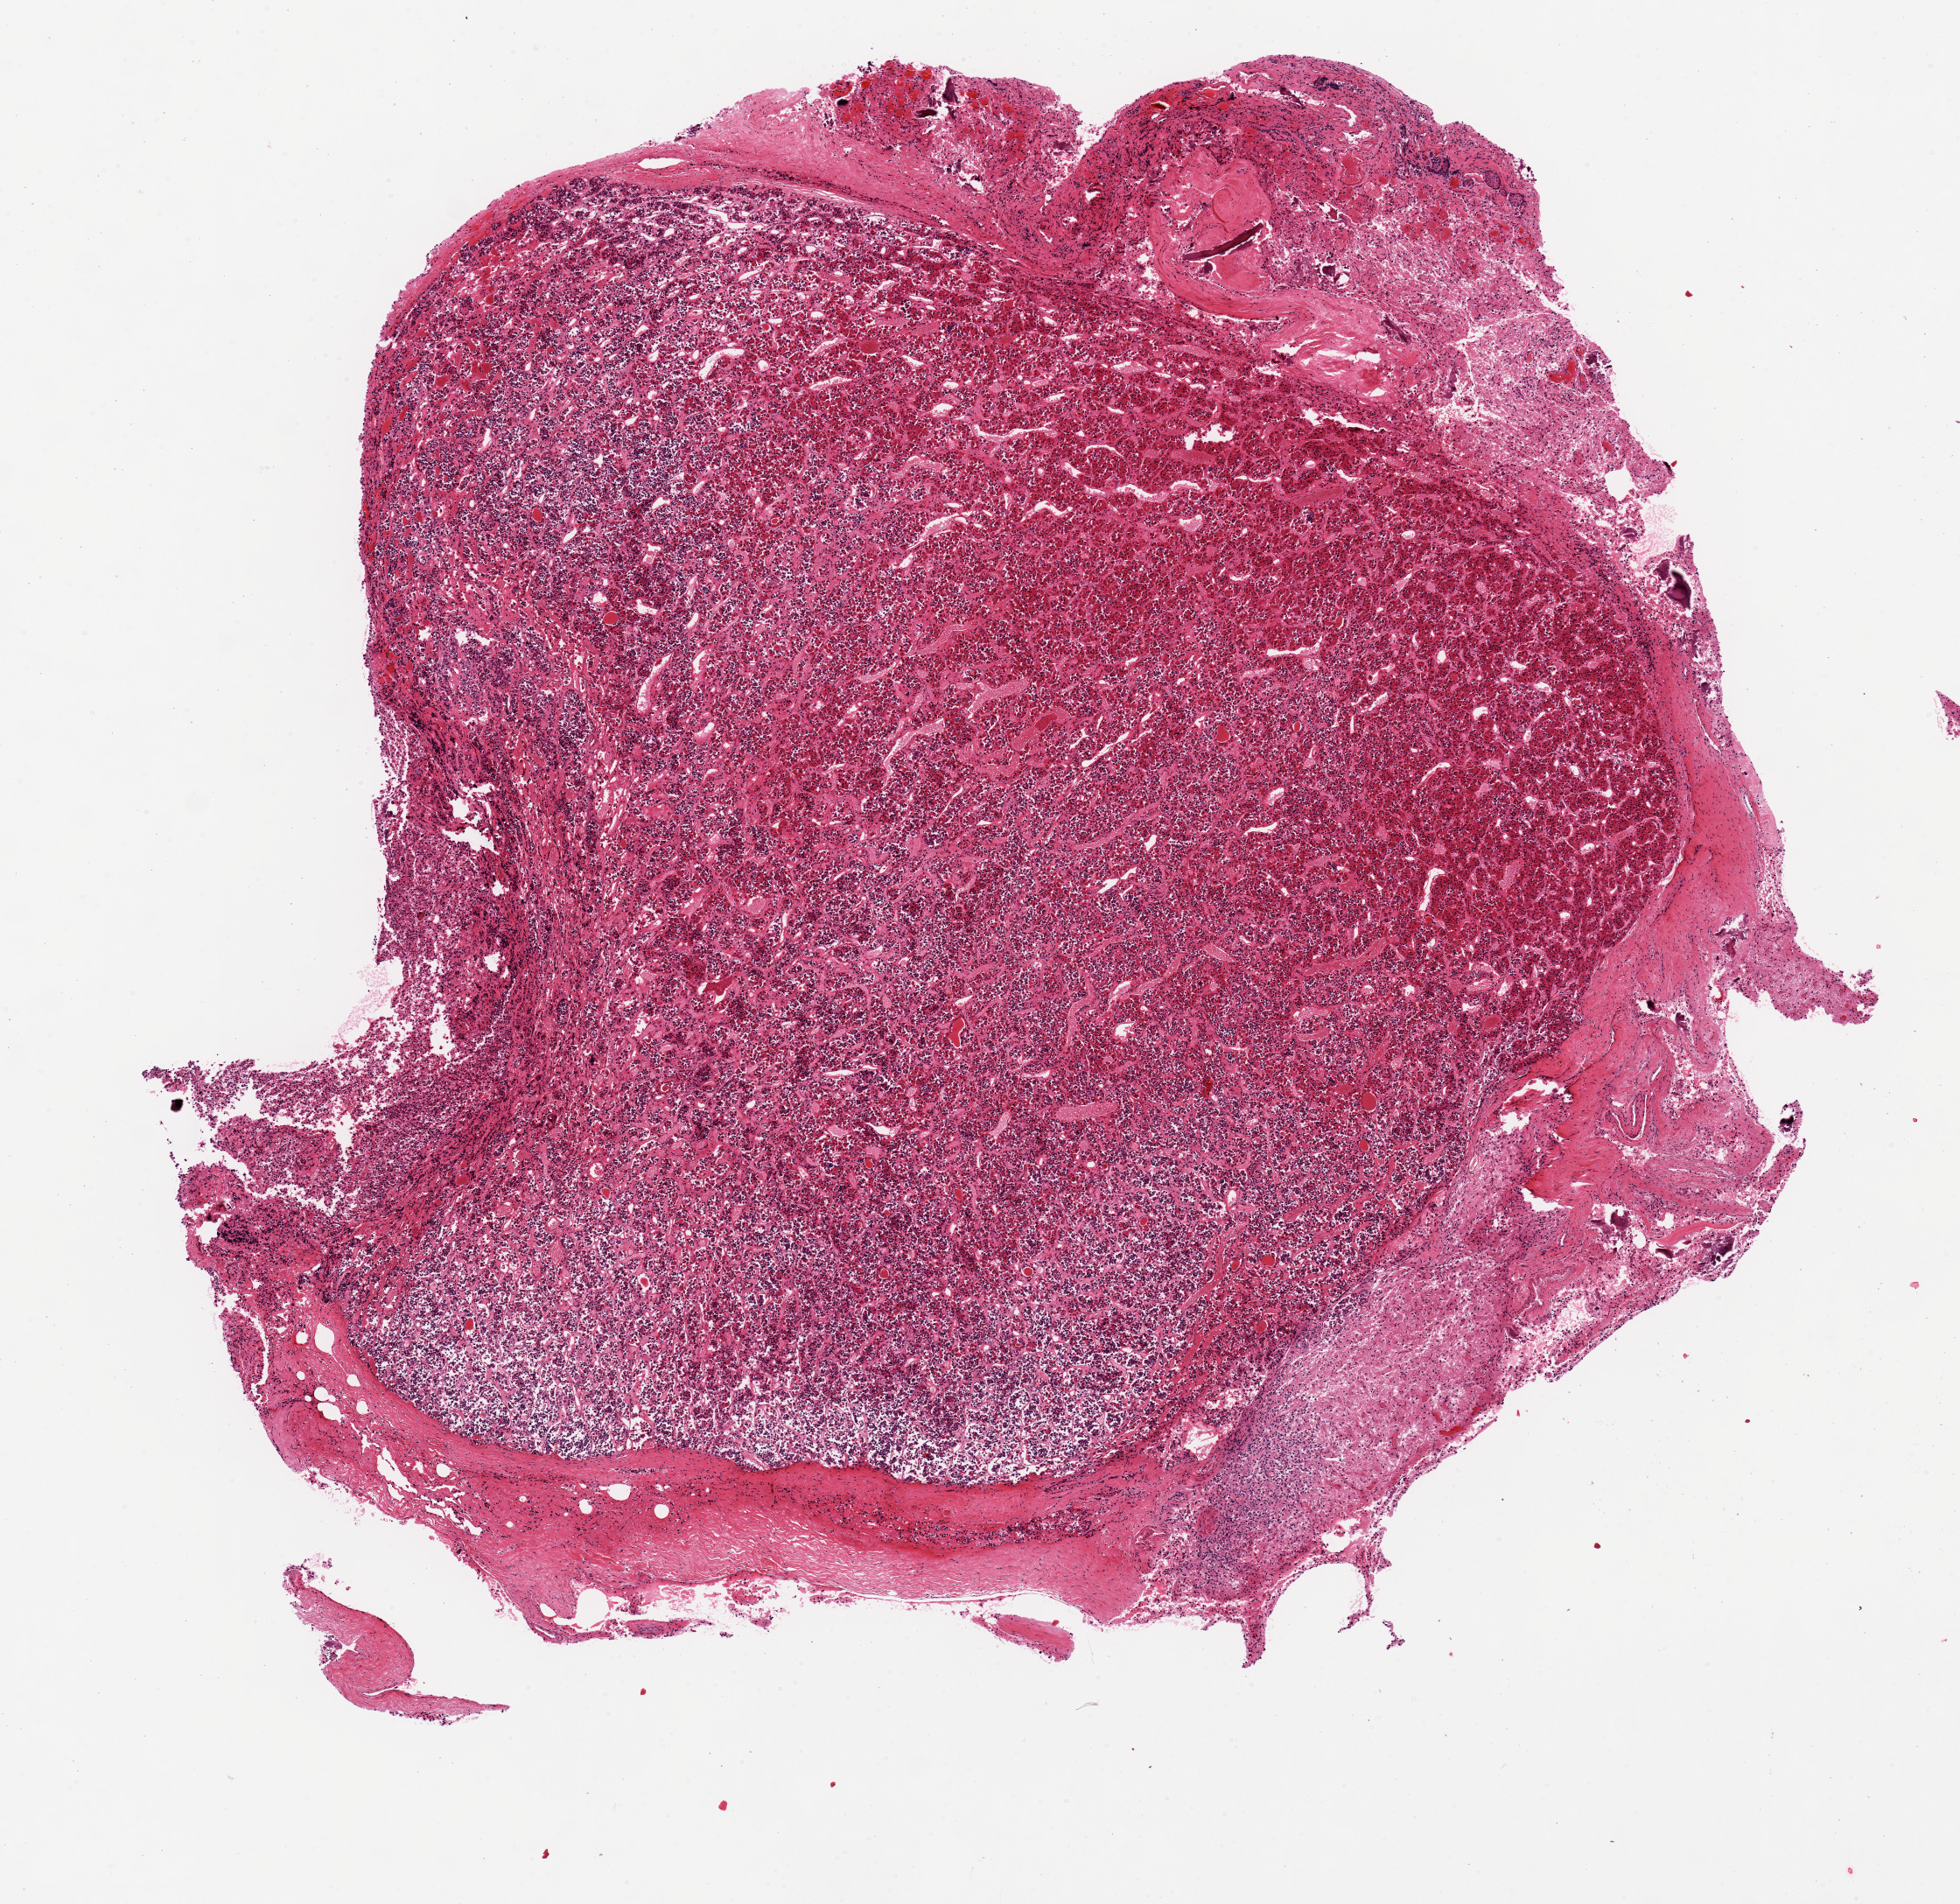
Hematoxylin and eosin (H&E) whole-slide image, low-resolution overview of the scanned area, about 8.9 x 8.6 mm, PAXgene-fixed, paraffin-embedded tissue, target tissue: pituitary, donor tissue sample.
Reviewer comment on this tissue sample: Mostly anterior pituitary; <10%.